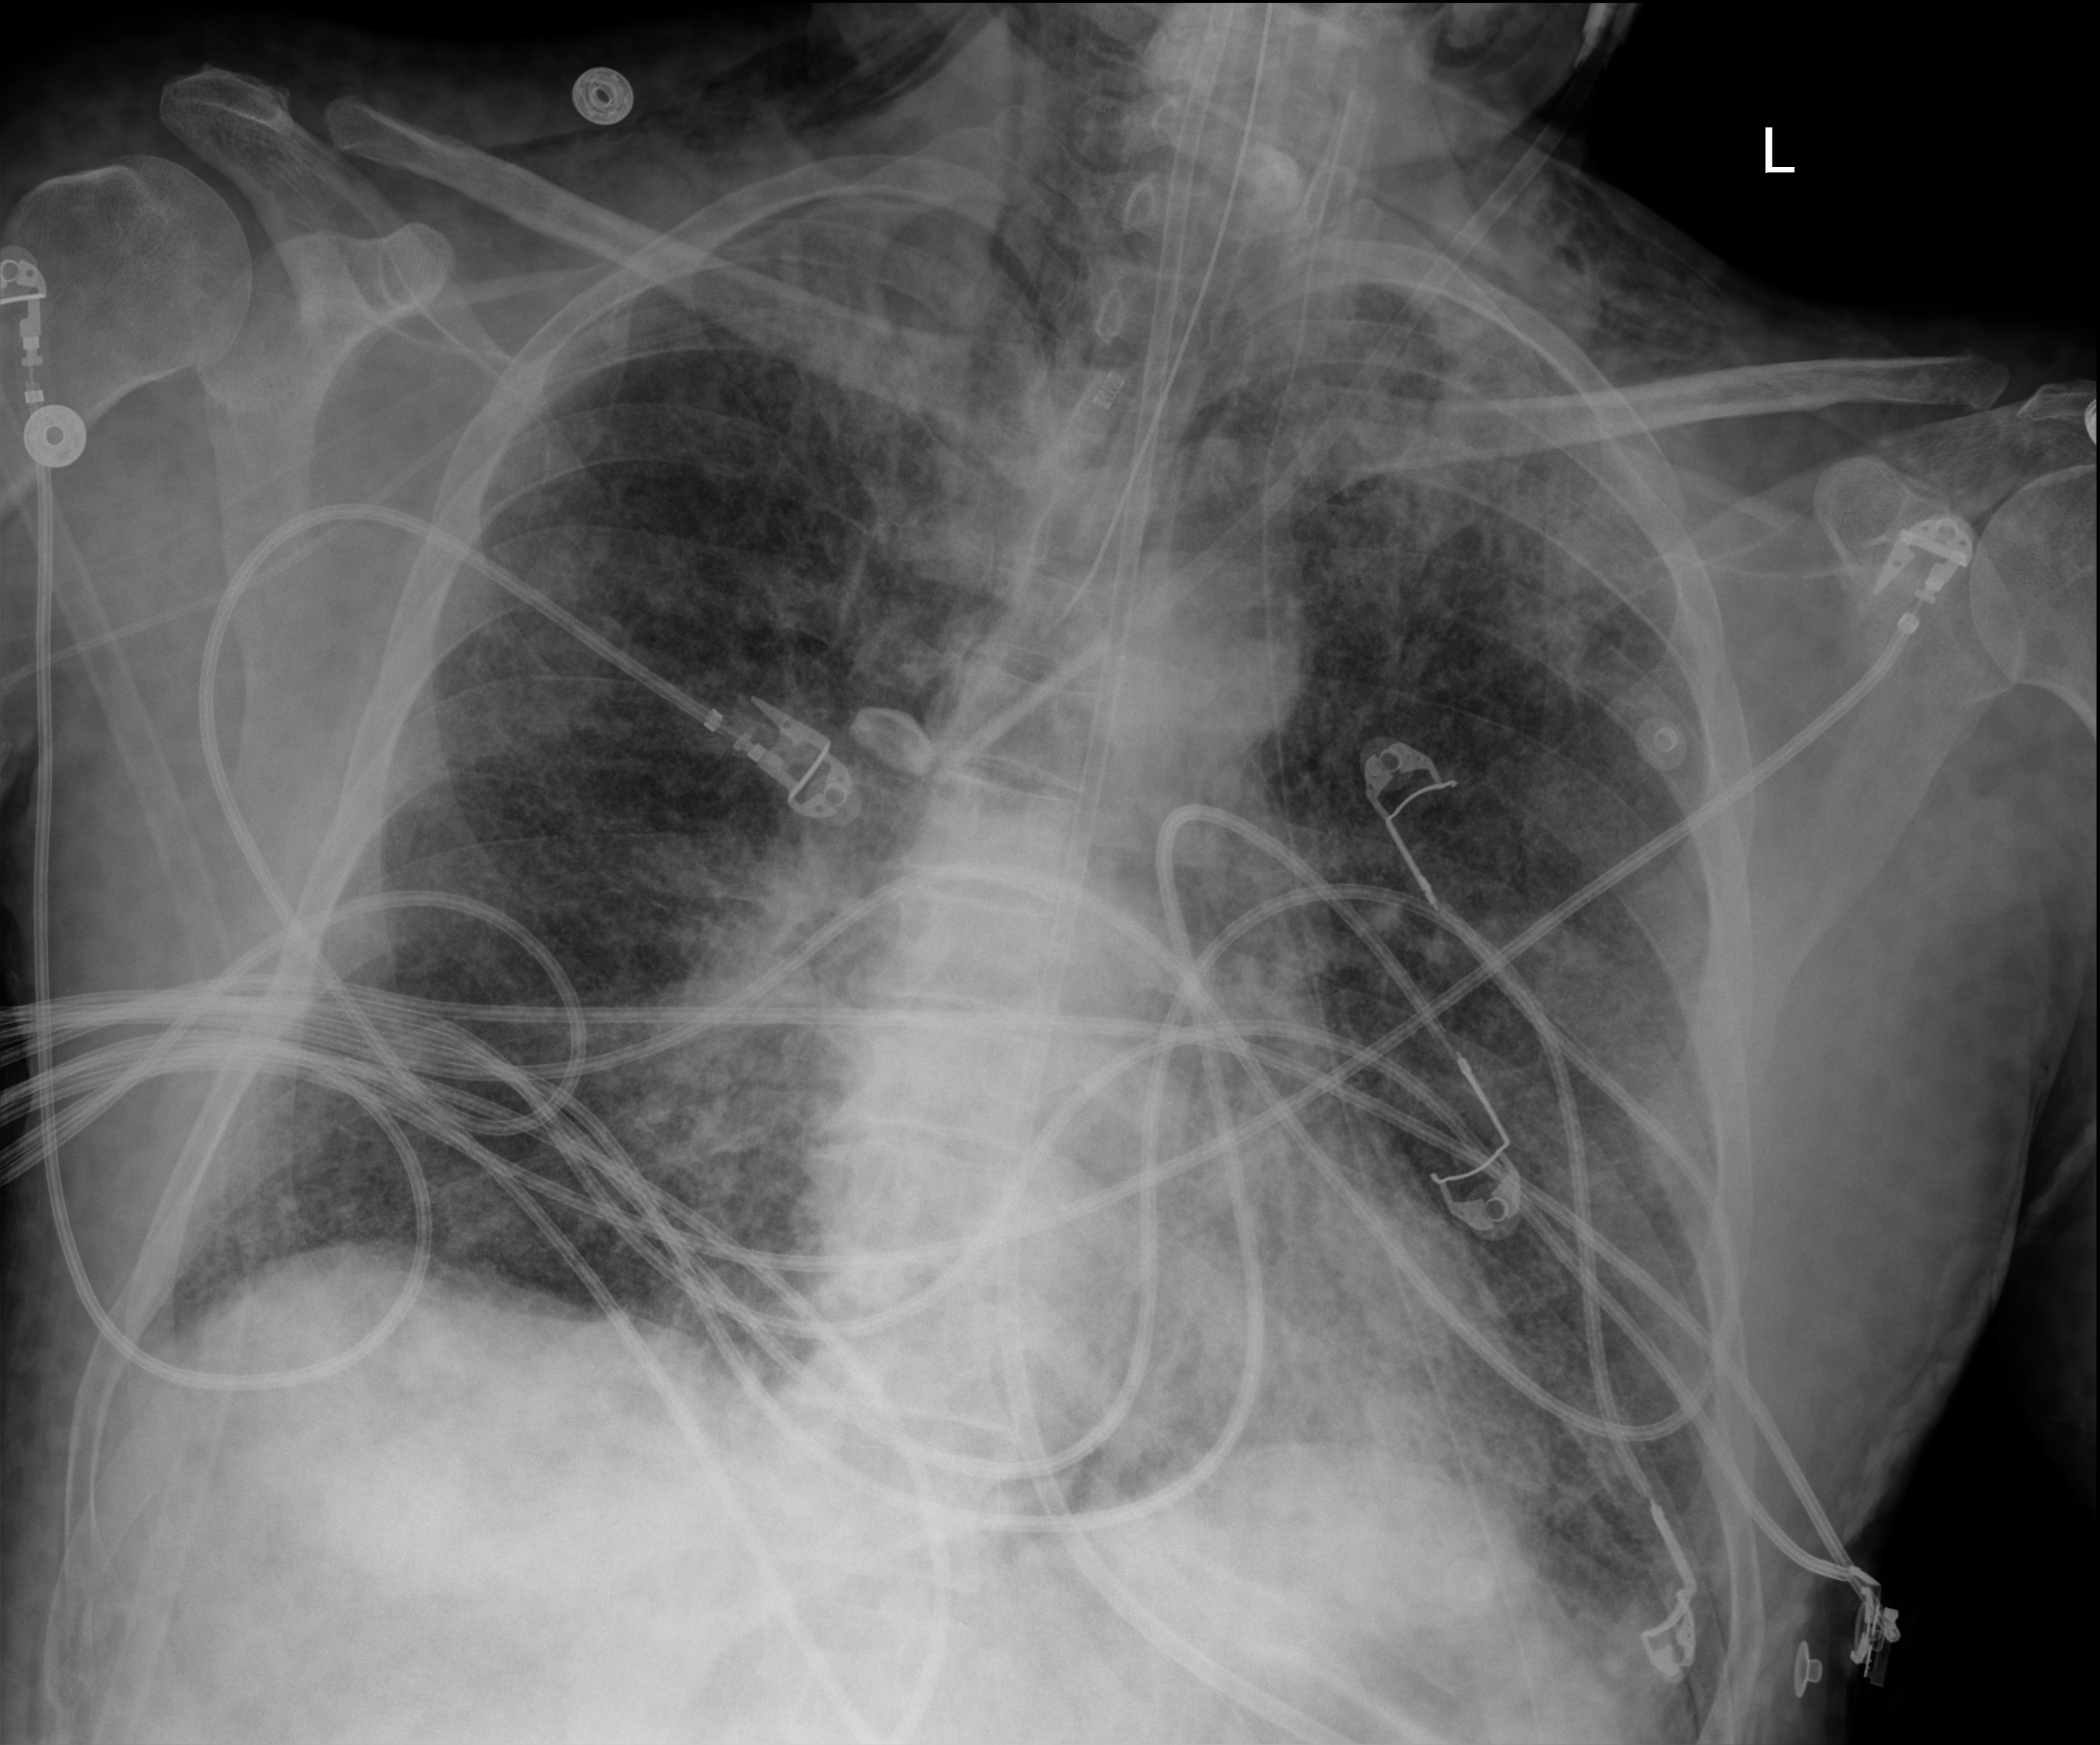
Chest X-ray (portable); anteroposterior (AP) projection. Male patient hospitalised with COVID-19, age 18–59 years.
From the hospital-stay record, not from the radiograph (when in the stay this image was taken is not recorded):
- diabetes (admission record): no